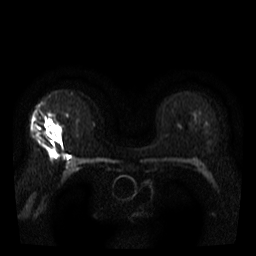
Breast MRI, one axial slice; position 24 of 40 along the scan axis; diffusion-weighted series; image 2 of 4 stored at this slice position (different b-values; order by instance number); 3 T; 5 mm slice thickness; 256 × 256 image matrix. Female patient.
Structures marked on this image (expert manual segmentation):
- tumour on diffusion-weighted imaging: bounding box [x1, y1, x2, y2] px = [48, 116, 61, 137]